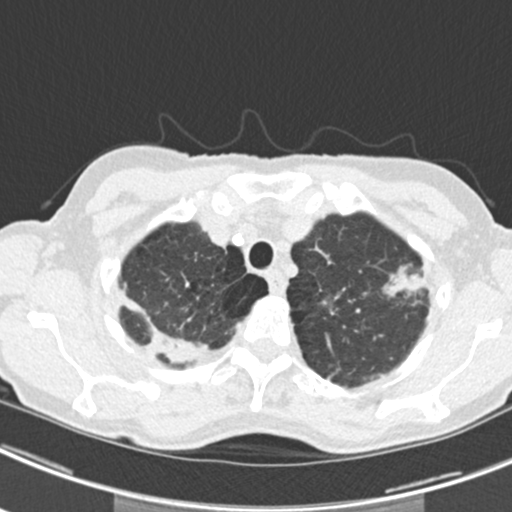
Low-dose screening chest CT, axial slice, second annual screen, lung window (W 1500 / L -600 HU), standard (soft-tissue) reconstruction kernel (B30f). Female, age 63 years at enrolment. Current smoker at enrolment.
- Lesion marked by an expert reader, box from (x=372, y=252) to (x=435, y=312) px.
- The screening reader recorded 9 non-calcified nodules or masses ≥4 mm on this exam (left upper lobe, right upper lobe, left upper lobe, left lower lobe, right middle lobe, left lower lobe, left lower lobe, right lower lobe, right lower lobe); which of them this box marks is not recorded.
- Official screen result: positive, other.
- Later outcome: lung cancer diagnosed 408 days after this screen — bronchiolo-alveolar adenocarcinoma, NOS, right upper lobe, right middle lobe, right lower lobe, left upper lobe, left lower lobe, moderately differentiated (G2), stage IV (AJCC 6th edition).